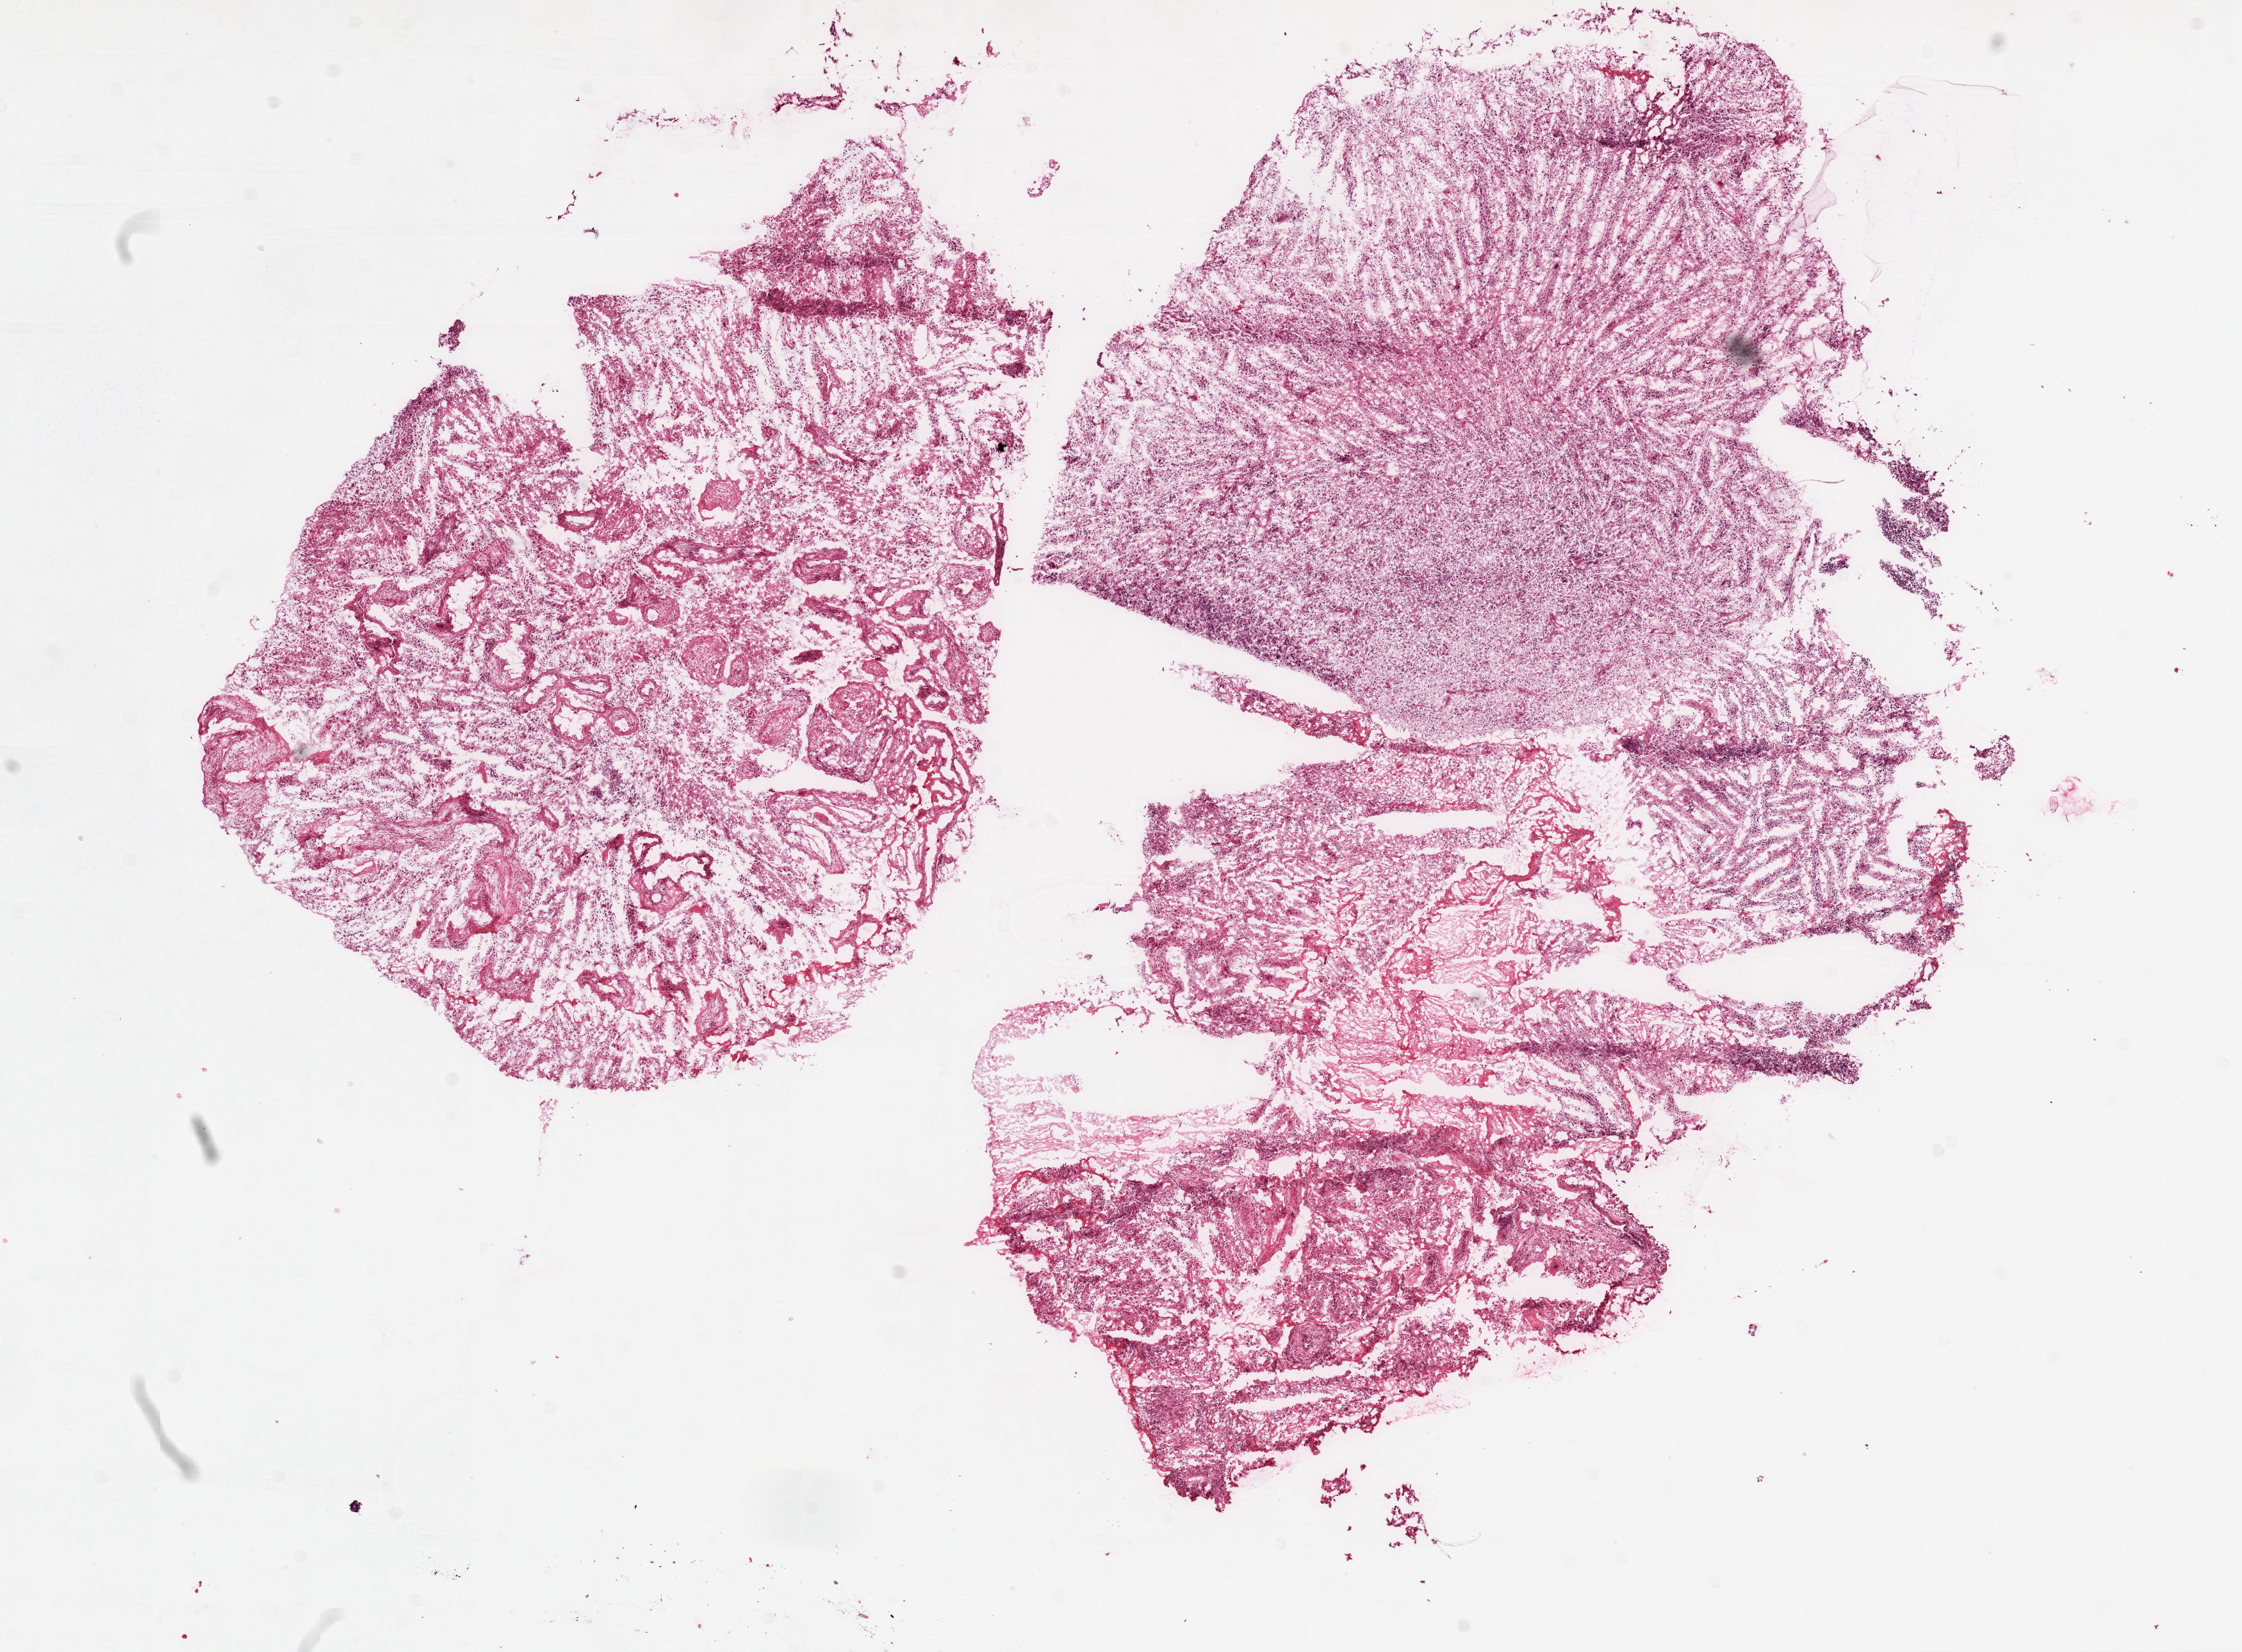
Hematoxylin and eosin (H&E) stained whole-slide image — whole scanned area (about 14.0 x 10.3 mm, slide scanned at 20x) shown as a low-resolution overview. Frozen section. Sample: primary tumour, brain. Patient: male, age at initial diagnosis 74 years. Pathologist review of this section (percent, as recorded): tumour cells 93%, tumour nuclei 85%, normal cells 0%, stromal cells 5%, necrosis 2%.
Histologic diagnosis: Glioblastoma.